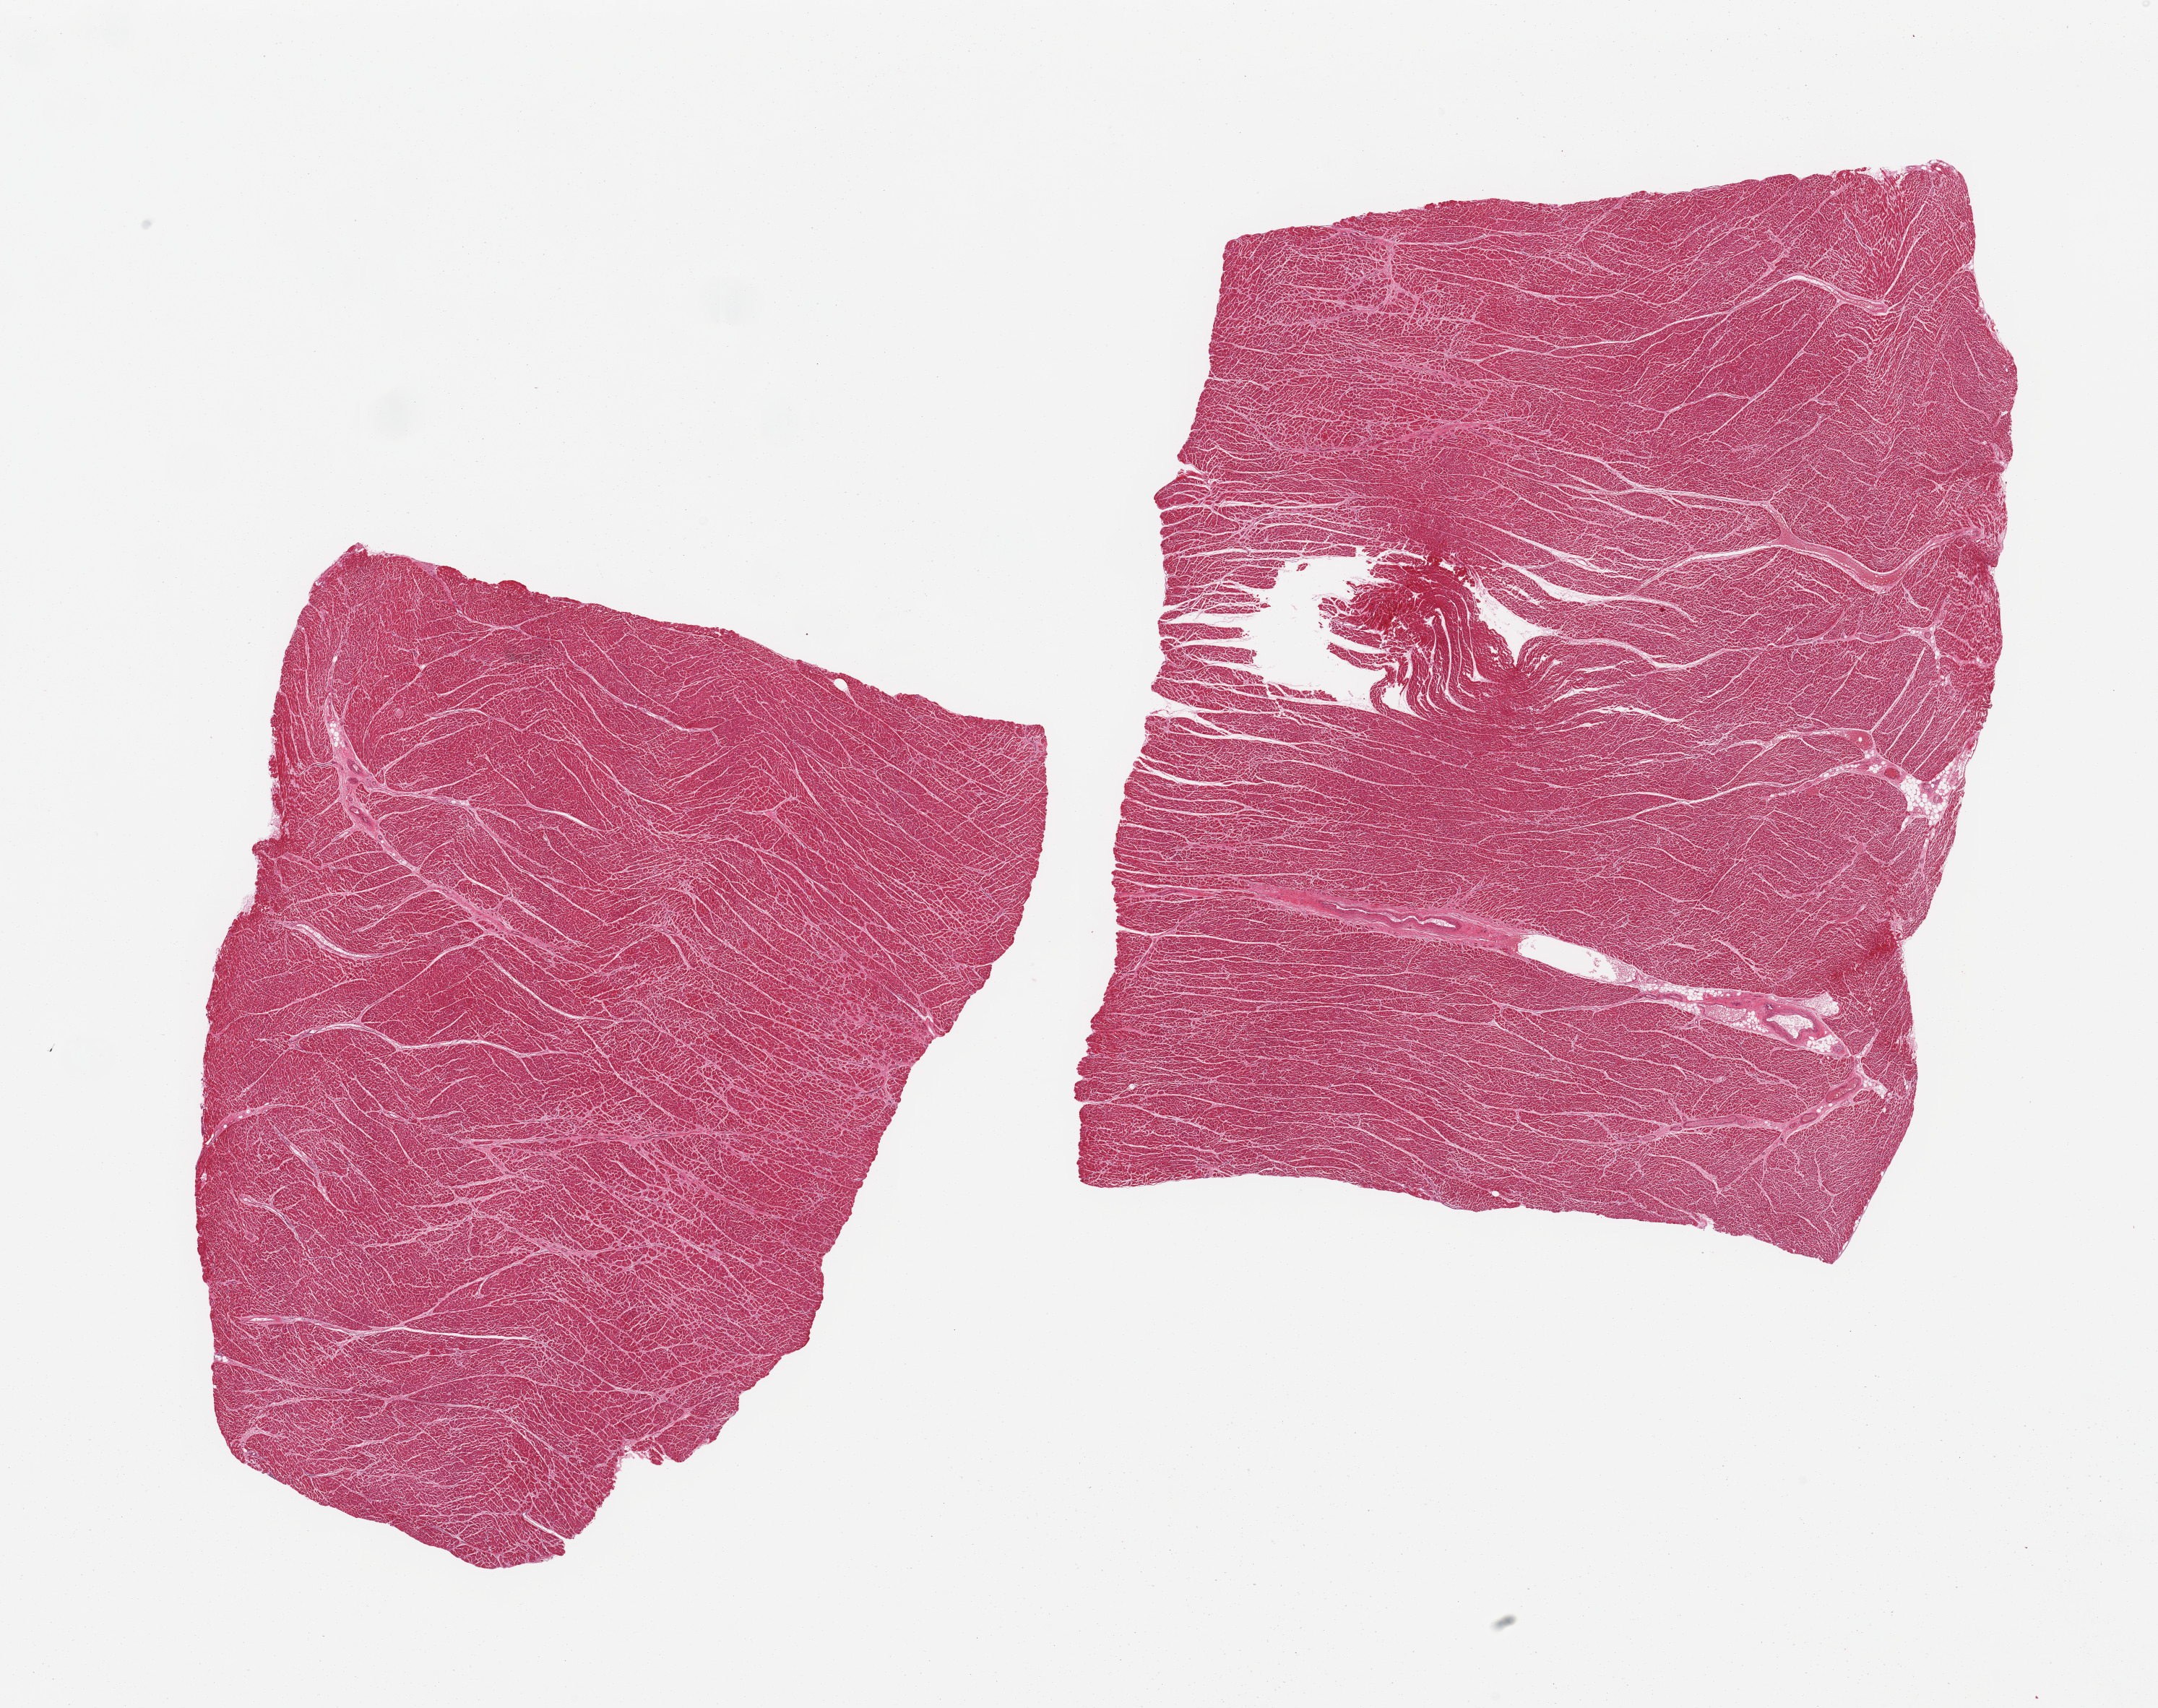
Hematoxylin and eosin (H&E) whole-slide image, a low-resolution overview of the entire scanned area, about 23.6 x 18.7 mm; PAXgene-fixed paraffin-embedded (PFPE) section; target tissue: heart; tissue donor sample. Donor: male.
Review note (as recorded): 2 pieces; no inflamed or scarred areas.